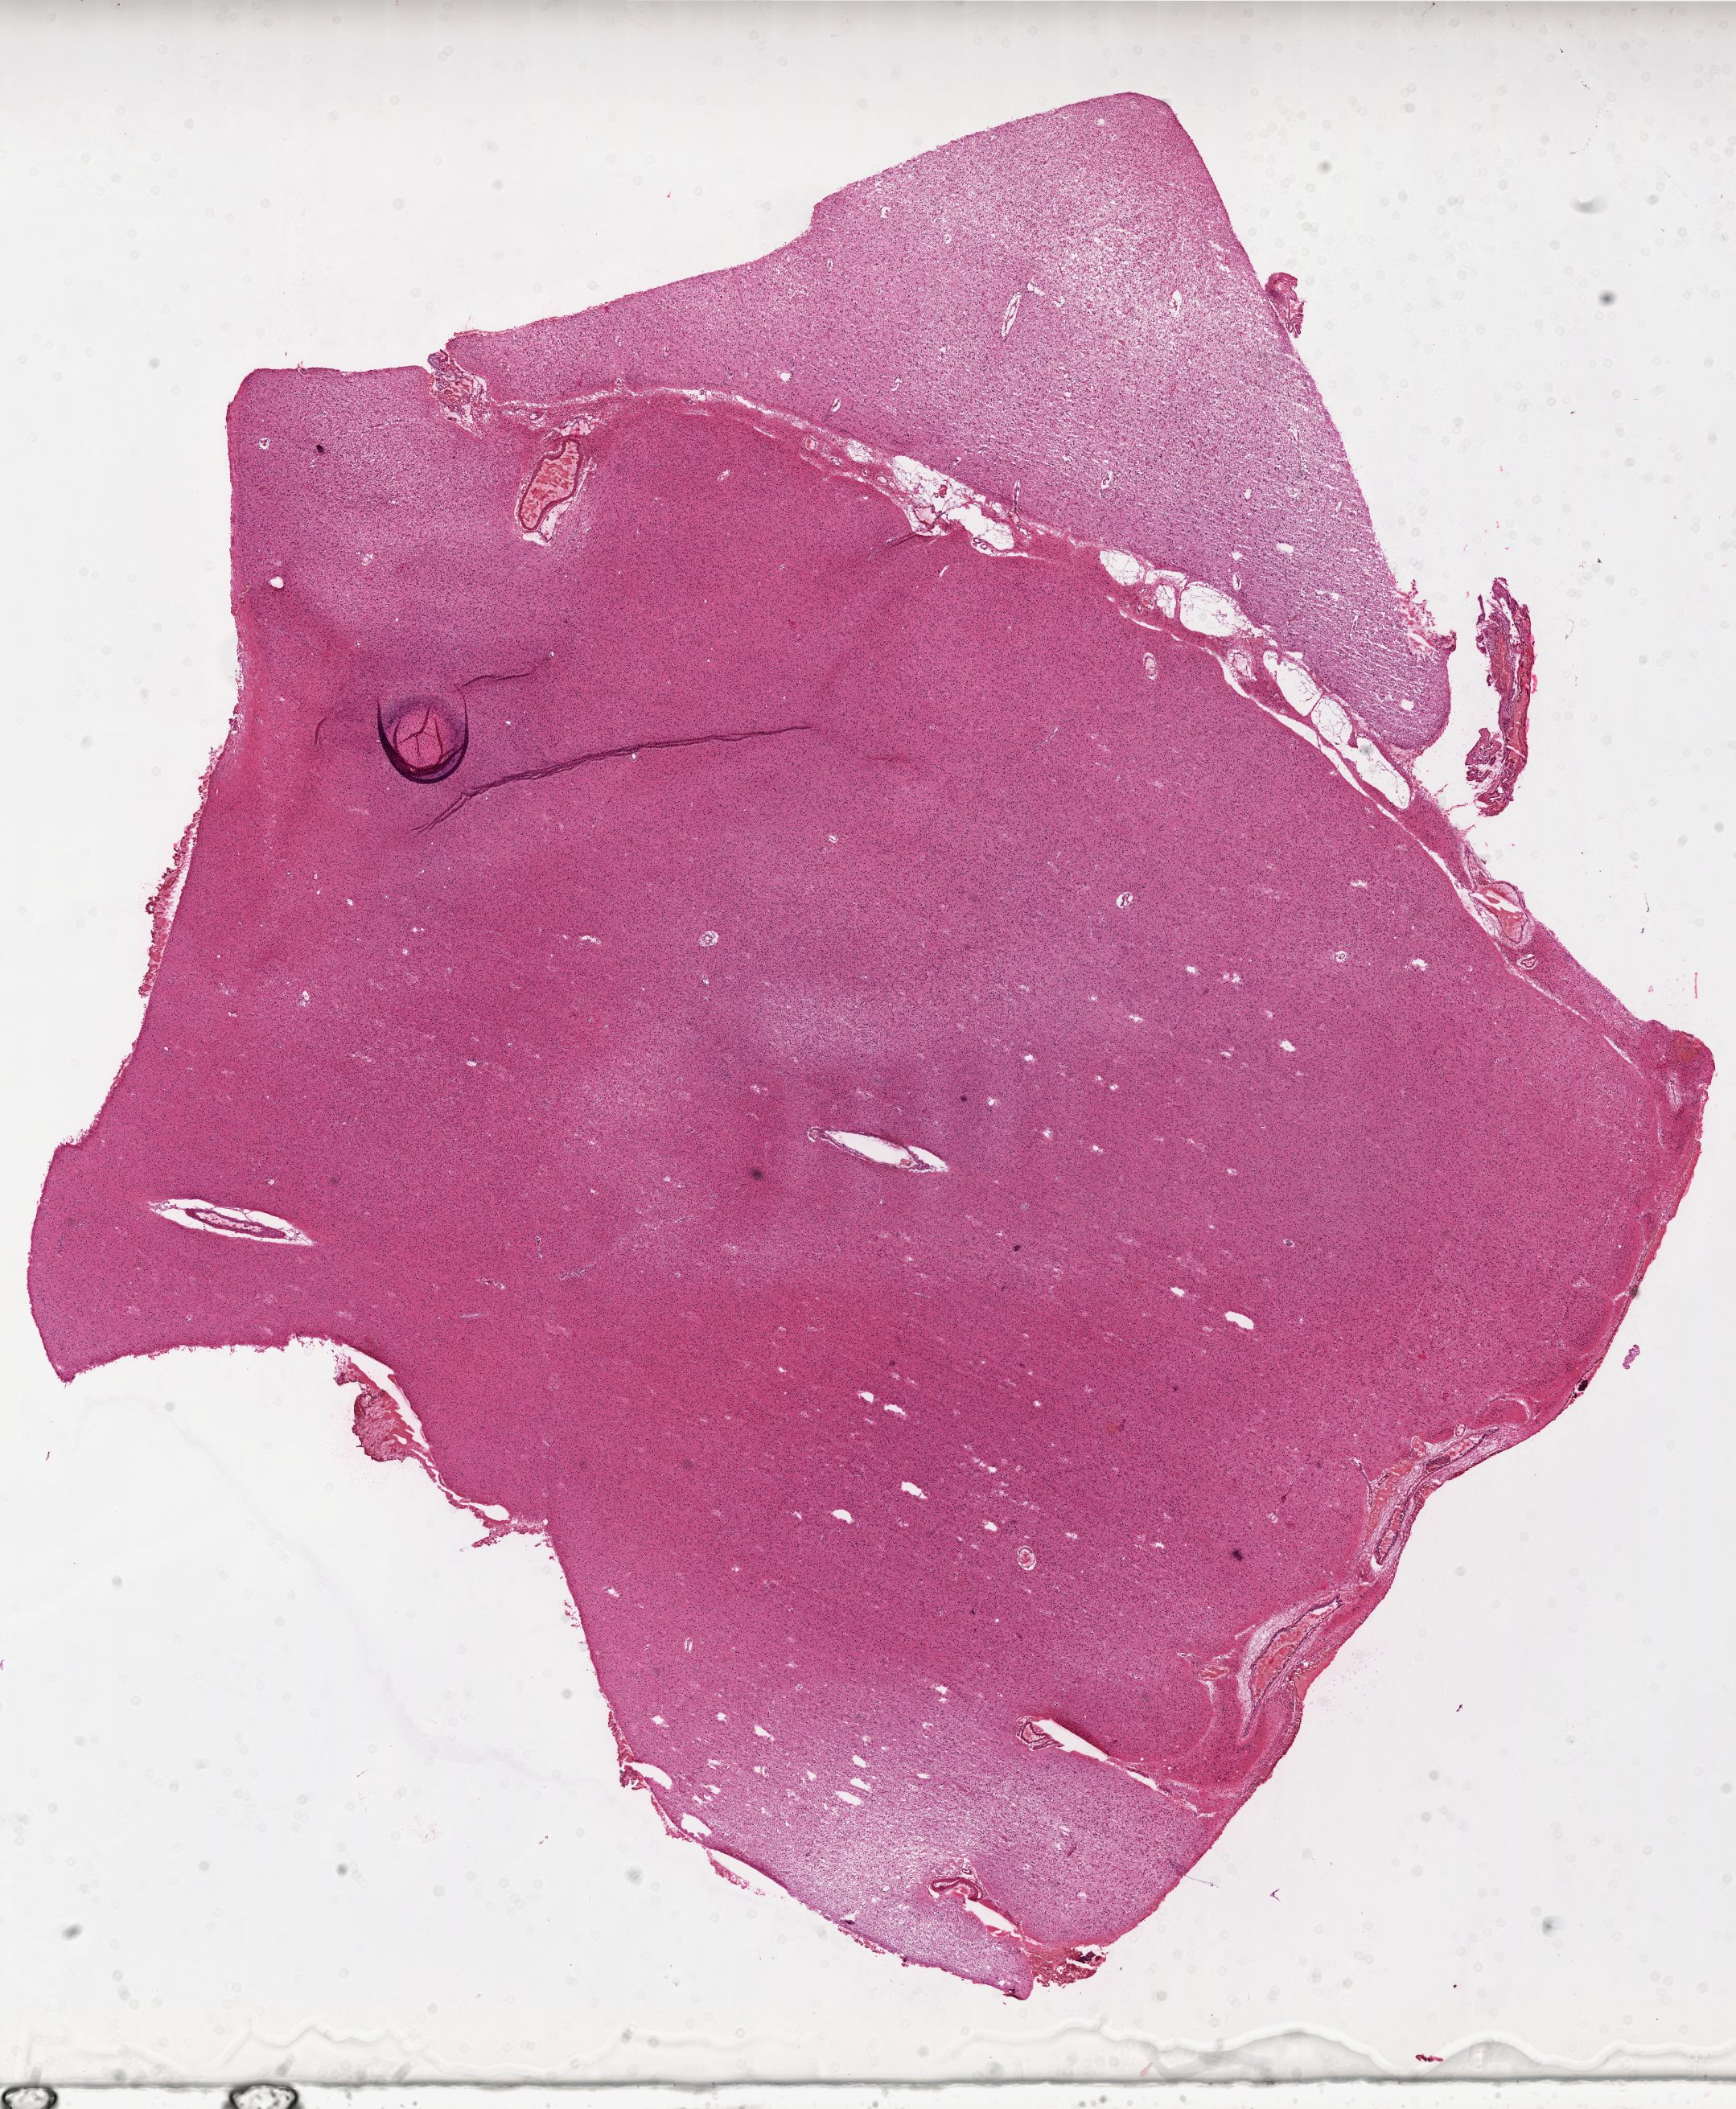
Digitized H&E-stained tissue section (whole slide), a low-resolution overview of the entire scanned area, about 17.4 x 21.1 mm (from a 20x scan); frozen section from the top of the tissue portion; sample: primary tumour, brain. Female patient; age at initial diagnosis 28 years. Composition of this section per pathologist review: tumour cells 80%, tumour nuclei 95%, normal cells 0%, stromal cells 20%, necrosis 0%.
Pathologic diagnosis: Glioblastoma.